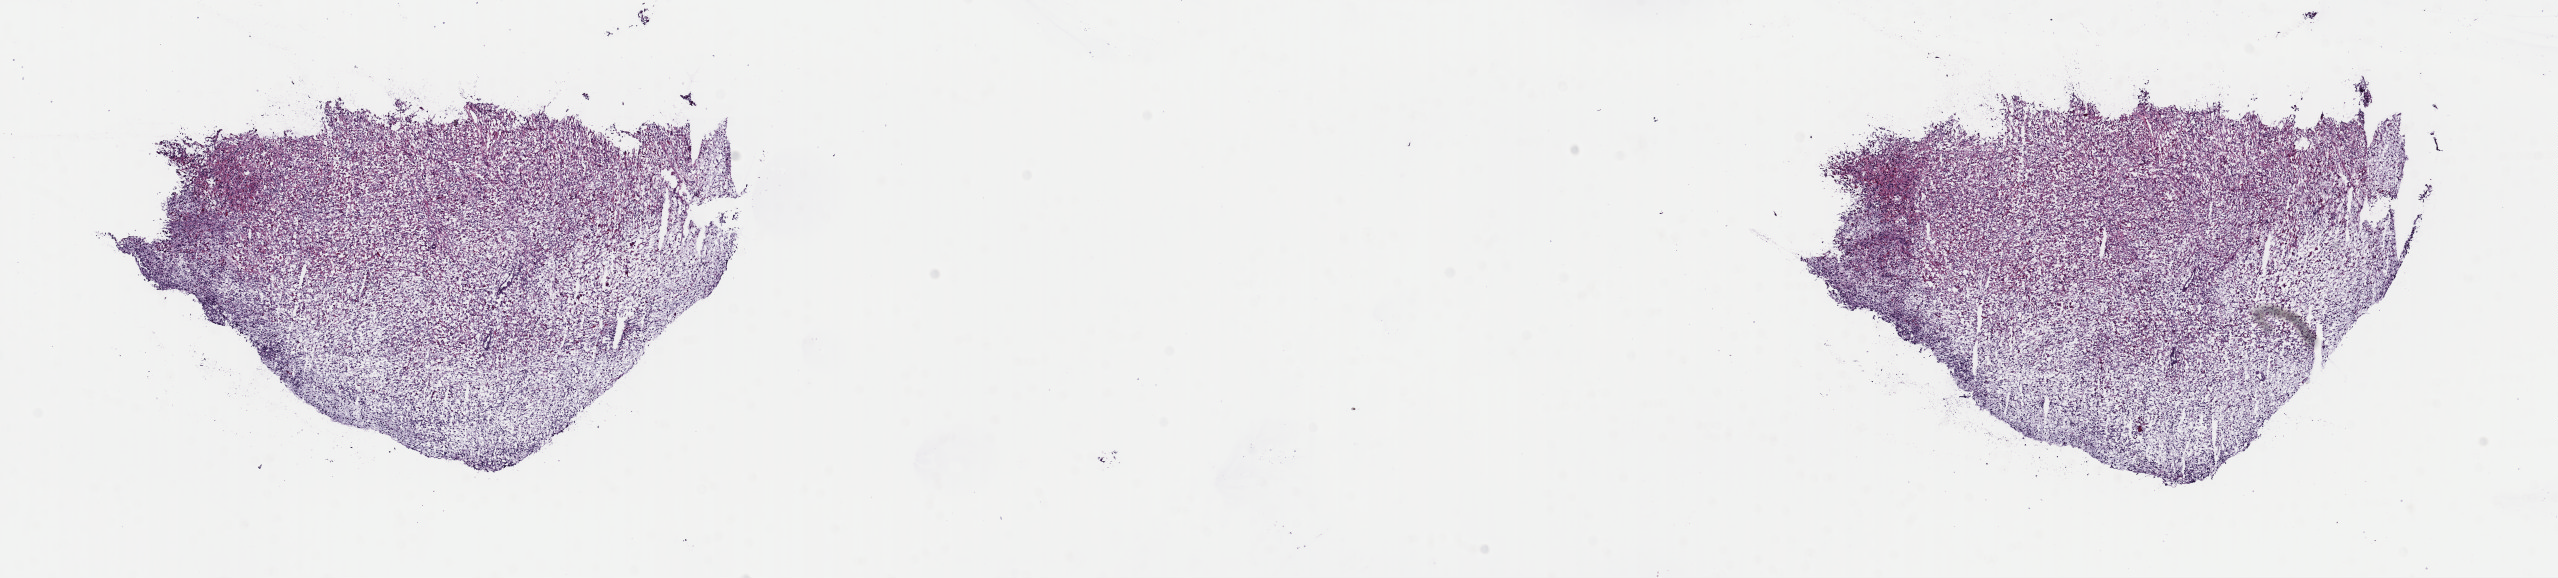
Digitized Hematoxylin and eosin (H&E) stained tissue section (whole slide) — a low-resolution overview of the entire scanned area, about 20.2 x 4.6 mm; frozen section from the top of the tissue portion; primary tumour sample from the uterus. Female, age 61 years at initial diagnosis. Slide review estimates, as recorded: tumour cells 100%, tumour nuclei 80%, normal cells 0%, stromal cells 0%, necrosis 0%. Infiltration values recorded for this section: lymphocyte infiltration 2%, monocyte infiltration 0%, neutrophil infiltration 0%.
- histologic diagnosis: Mullerian mixed tumor (corpus uteri)
- FIGO stage: IIA